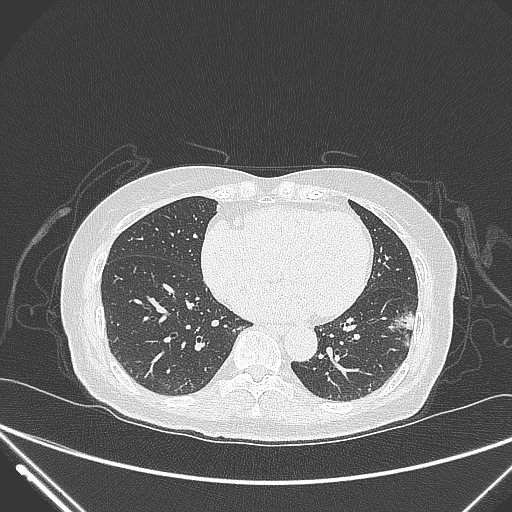
Chest CT, one axial slice. Position 114 of 310 along the scan axis. Lung window (W 1500 / L -600 HU). 1 mm slice thickness. 512 × 512 image matrix. Patient: female, 82 years. From the clinical record (not read from this slice): clinical TNM (as recorded): T1c N0 M0; histopathological grade: G2.
Annotated regions visible in this slice (rectangle marked by the reading radiologist):
- lung tumour (recorded histology: adenocarcinoma): bounding box <390,303,418,348> (left, top, right, bottom; pixels)